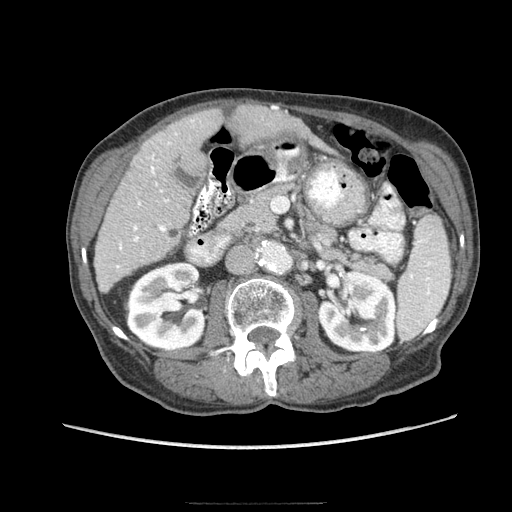
Contrast-enhanced abdominal CT (liver protocol), one axial slice; position 33 of 83 along the scan axis; soft-tissue window (W 400 / L 40 HU); 2.5 mm slice thickness; 512 × 512 image matrix. From the clinical record (not read from this slice): diagnosis: hepatocellular carcinoma (patient treated with transarterial chemoembolisation; whether this scan precedes or follows treatment is not stated here); TNM stage (as recorded): Stage-I; Child-Pugh class: A.
Structures marked on this image (semi-automatically segmented with operator editing):
- liver parenchyma outside the tumour (the mass and vessels are separate outlines, so this box may not span the whole liver): box from (x=94, y=104) to (x=304, y=292) px
- liver vessels: (x=116, y=106)–(x=278, y=268)